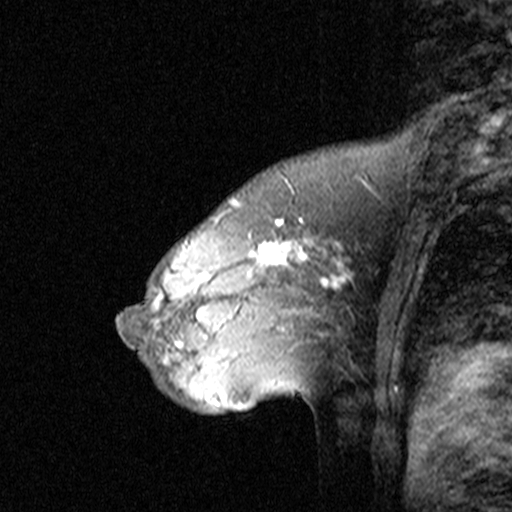
Breast MRI (dynamic contrast-enhanced), one sagittal slice; position 29 of 44 along the scan axis; dynamic contrast-enhanced study with each time point stored as its own series, time point 2 of 3 at this slice position (early post-contrast, ordered by acquisition time); 1.5 T; TE 4.5 ms, TR 11 ms; 3 mm slice thickness; 512 × 512 image matrix, field of view 200 × 200 mm. Patient: female, 46 years. Case-level facts recorded for this patient, not image findings: setting: breast cancer imaged before/during neoadjuvant chemotherapy; receptor status: HER2-positive.
Outlined on this slice (semi-automatic segmentation, software-assisted and operator-edited):
- analysis volume of interest (the breast-tissue region the enhancement analysis was run in; not a lesion): bounding box (x1, y1, x2, y2) in pixels: (144, 172, 359, 393)
- tumour enhancement mask (voxels above the 90 % enhancement threshold inside the analysis volume of interest): (154, 218, 352, 348)